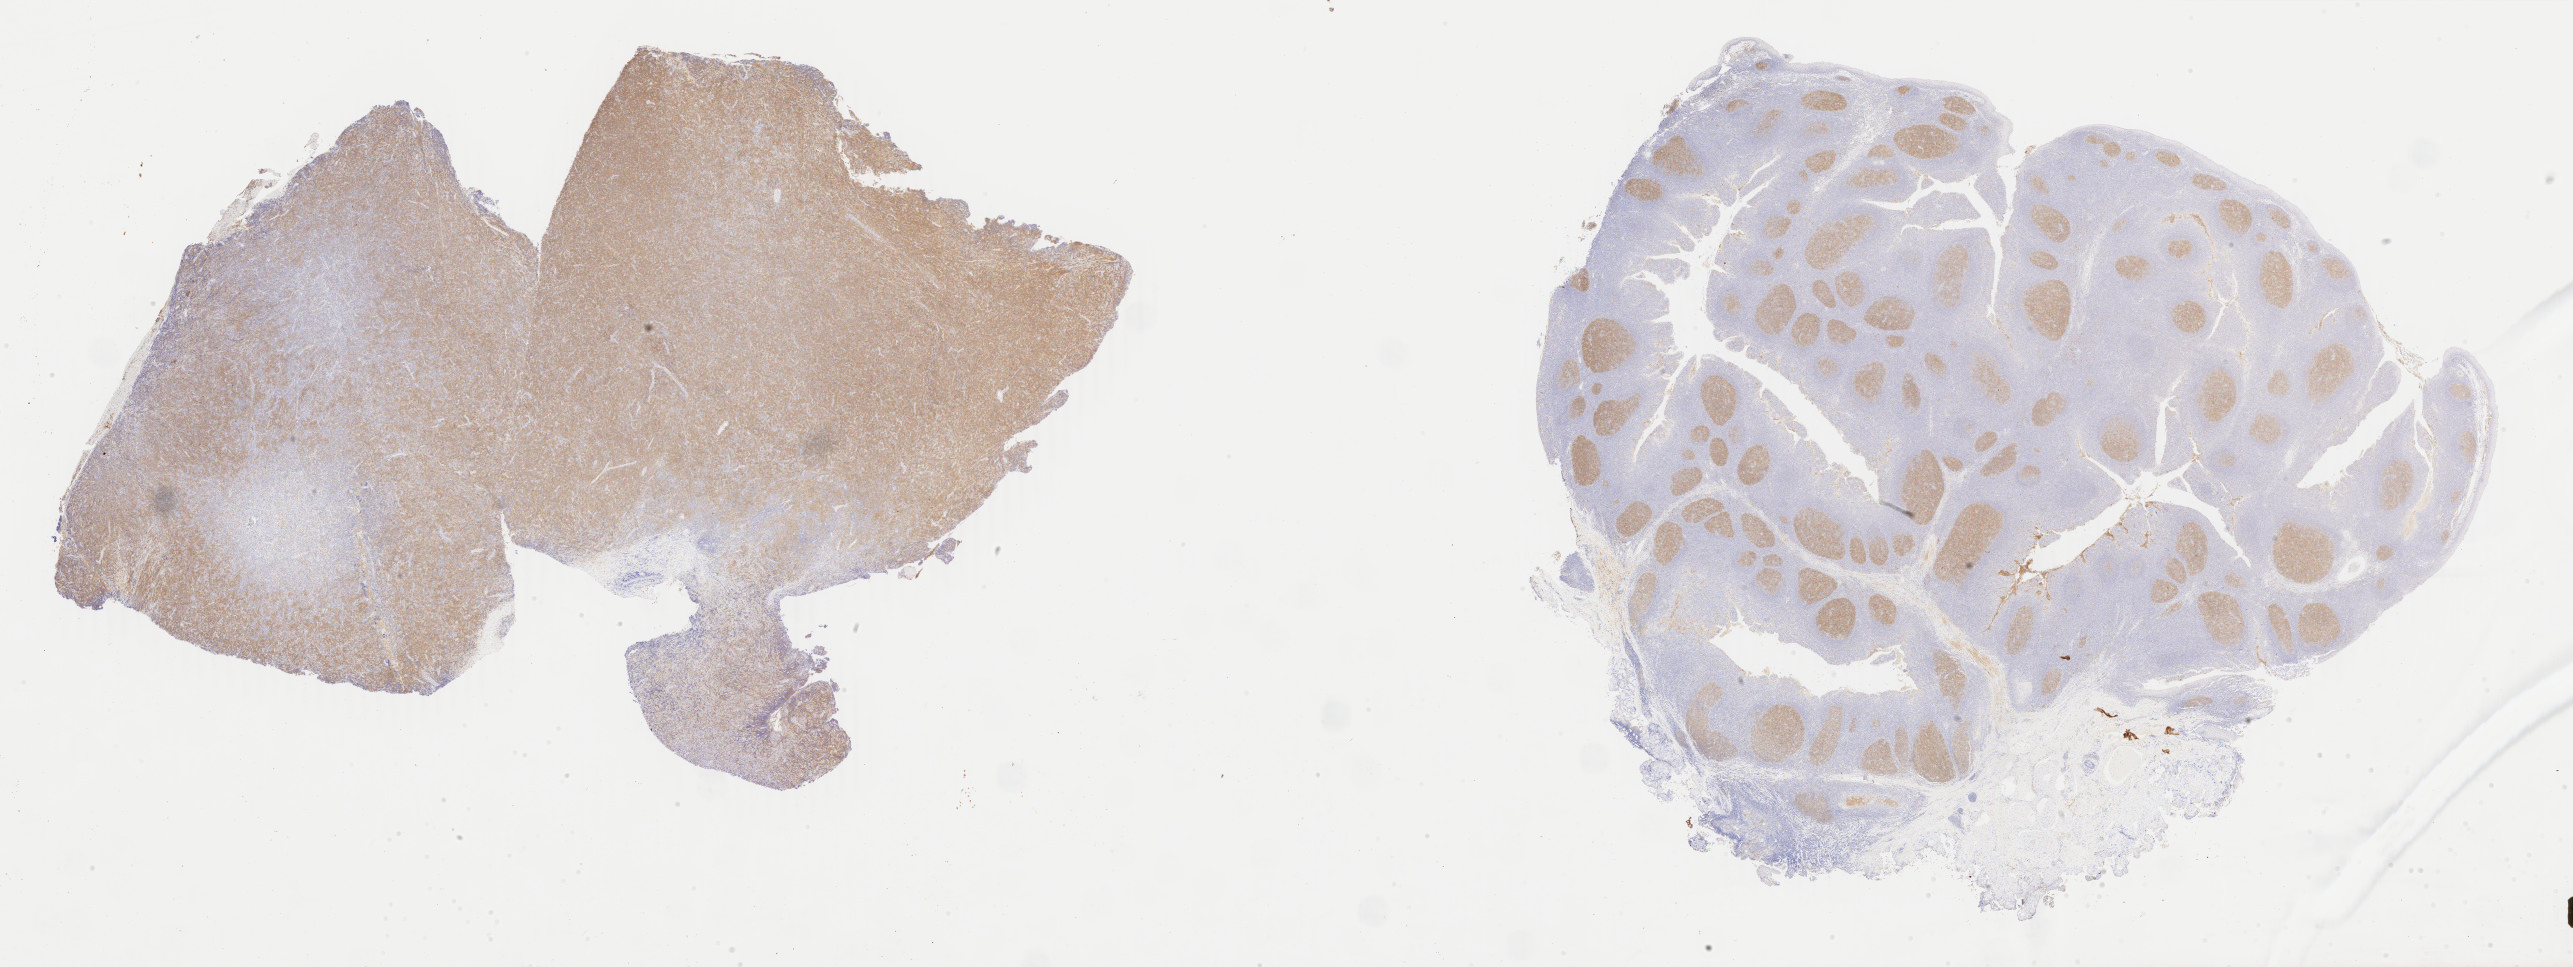
Immunohistochemistry (IHC) whole-slide image stained for CD10, low-resolution overview of the scanned area, about 40.9 x 15.4 mm; tumor tissue. Patient: male, age at initial diagnosis 7 years.
Histologic diagnosis: Diffuse large B-cell lymphoma, NOS.